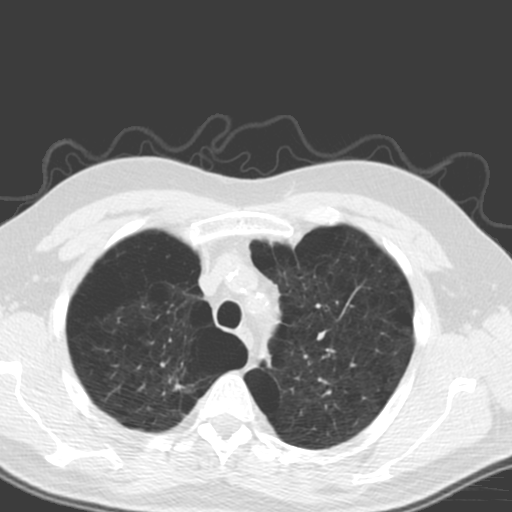
Low-dose screening chest CT, one axial slice; slice 137 of 173 in the series (ordered by position); 120 kVp; lung window (W 1500 / L -600 HU); 512 × 512 image matrix, field of view 340 × 340 mm.
Annotated regions visible in this slice (outlined manually by an expert reader):
- lesion 1 (tumor, upper lobe of right lung): bounding box (x1, y1, x2, y2) in pixels: (174, 383, 184, 390)